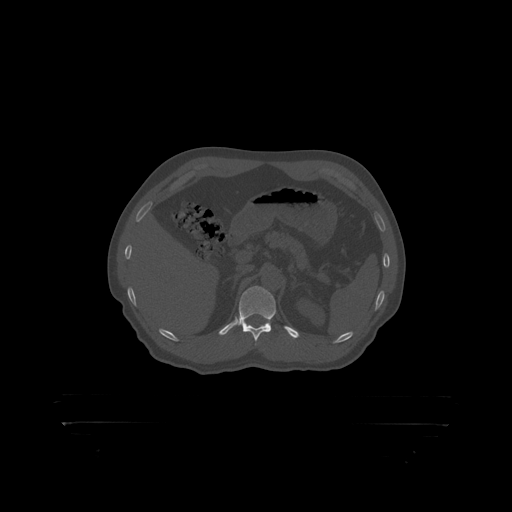
CT including the spine, one axial slice; slice 350 of 399 in the series (ordered by position); bone window (W 1800 / L 400 HU); 1.25 mm slice thickness; 512 × 512 image matrix. Patient: male, 46 years. From the clinical record (not read from this slice): primary cancer: skin.
Outlined on this slice (semi-automatically segmented with operator editing):
- T12 vertebra: box from (x=239, y=286) to (x=277, y=319) px